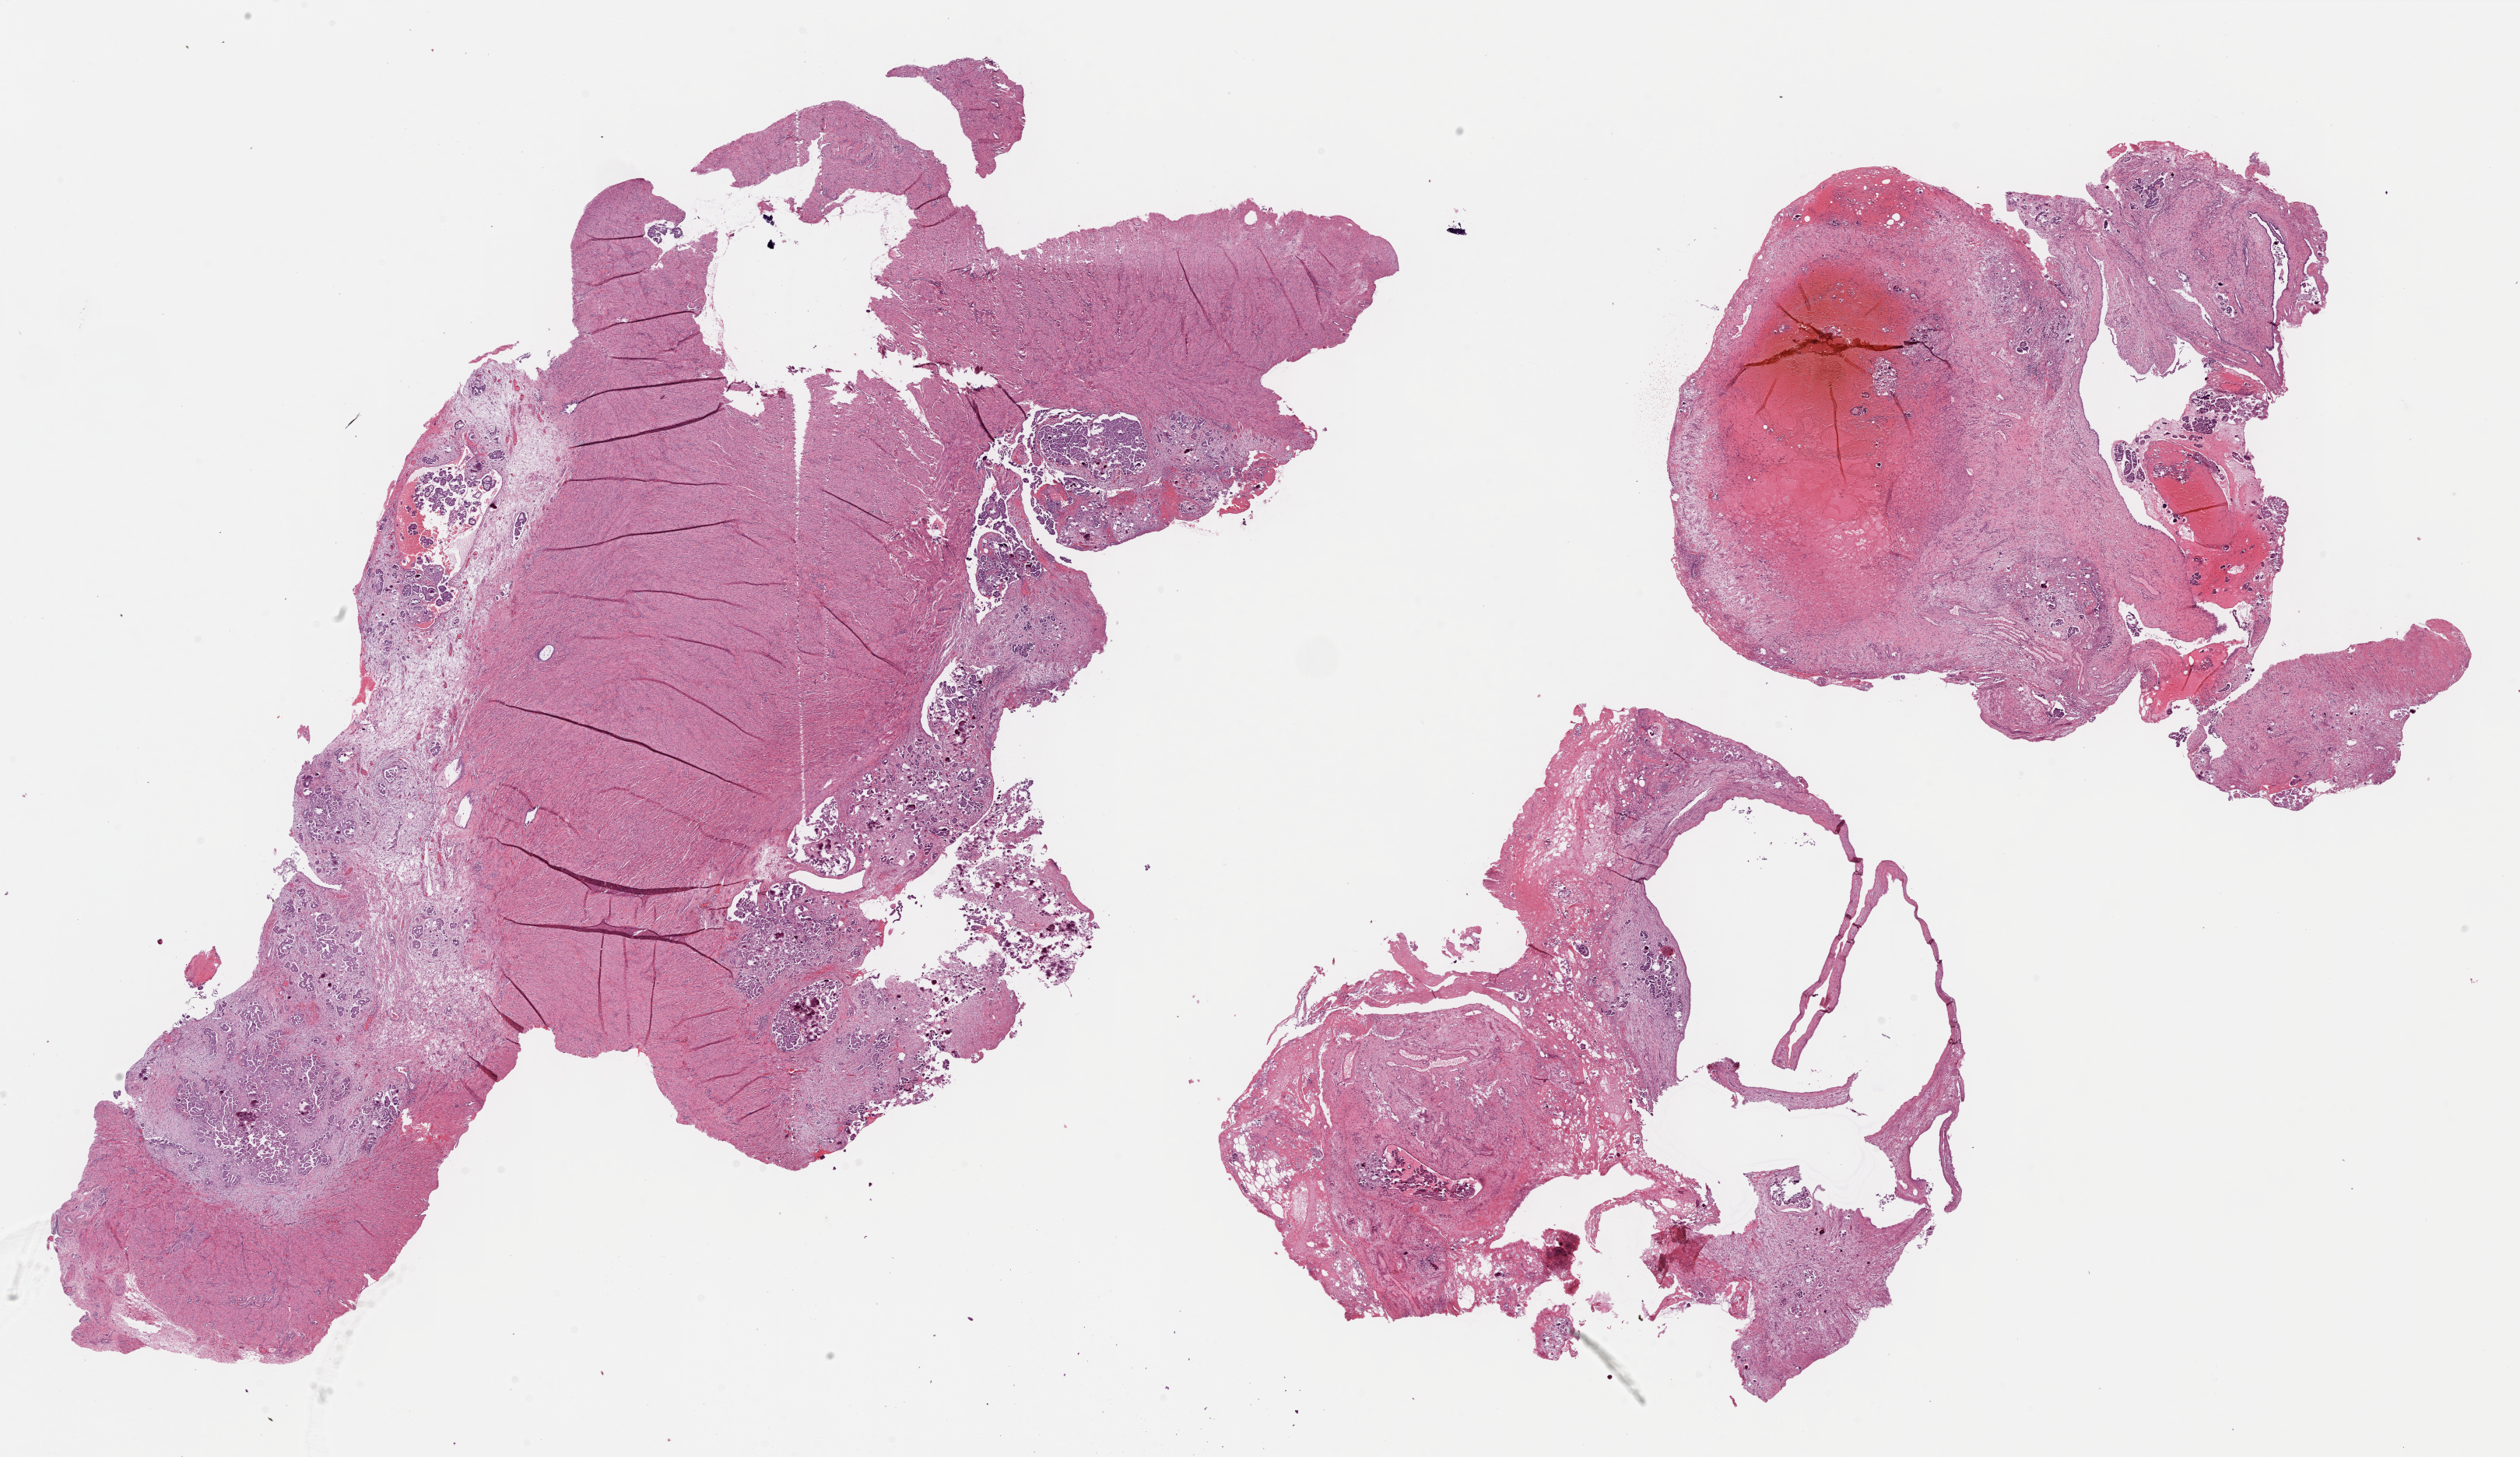
Digitized H&E-stained tissue section (whole slide) — shown as a low-resolution overview of the whole scanned area (about 26.1 x 15.1 mm); formalin-fixed paraffin-embedded (FFPE) diagnostic section; ovary, primary tumour sample. Female patient; age at initial diagnosis 38 years. Histologic grade: G3 (poorly differentiated).
• pathologic diagnosis: Serous cystadenocarcinoma, NOS
• laterality: bilateral
• FIGO stage: IIIC